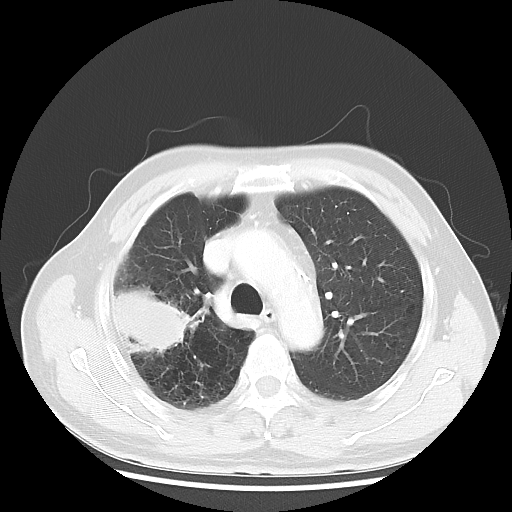
Chest CT, one axial slice. Position 36 of 50 along the scan axis. Reconstruction kernel LUNG. 120 kVp. Lung window (W 1500 / L -600 HU). 5 mm slice thickness. 512 × 512 image matrix, field of view 360 × 360 mm. Patient: male, 69 years. Case-level facts recorded for this patient, not image findings: clinical TNM (as recorded): T3 N0 M0.
Outlined on this slice (bounding box drawn by a radiologist):
- lung tumour (recorded histology: adenocarcinoma): box from (x=111, y=277) to (x=198, y=357) px